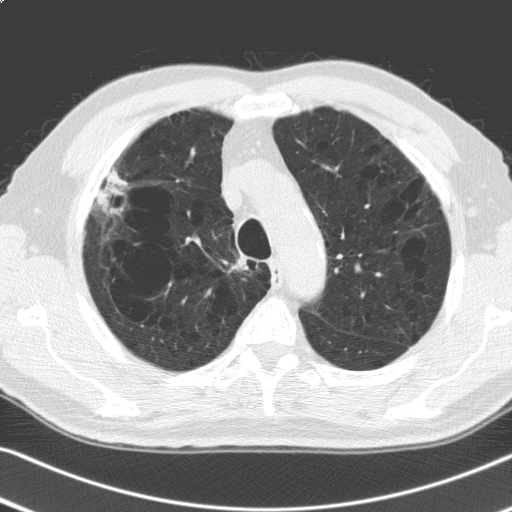
Low-dose screening chest CT, axial slice; second annual screen; lung window (W 1500 / L -600 HU); standard (soft-tissue) reconstruction kernel (C); slice 37 of 168 in the series; 512 × 512 image matrix. Male, age 69 years at enrolment. Former smoker at enrolment.
Expert reader's lesion annotation, box from (x=88, y=166) to (x=133, y=220) px. The screening reader recorded 6 non-calcified nodules or masses ≥4 mm on this exam (right upper lobe, right upper lobe, right lower lobe, lingula, left lower lobe, left lower lobe); which of them this box marks is not recorded. Later outcome: lung cancer diagnosed 91 days after this screen — adenosquamous carcinoma, right upper lobe, poorly differentiated (G3), stage IV (AJCC 6th edition), 30 mm at pathology.